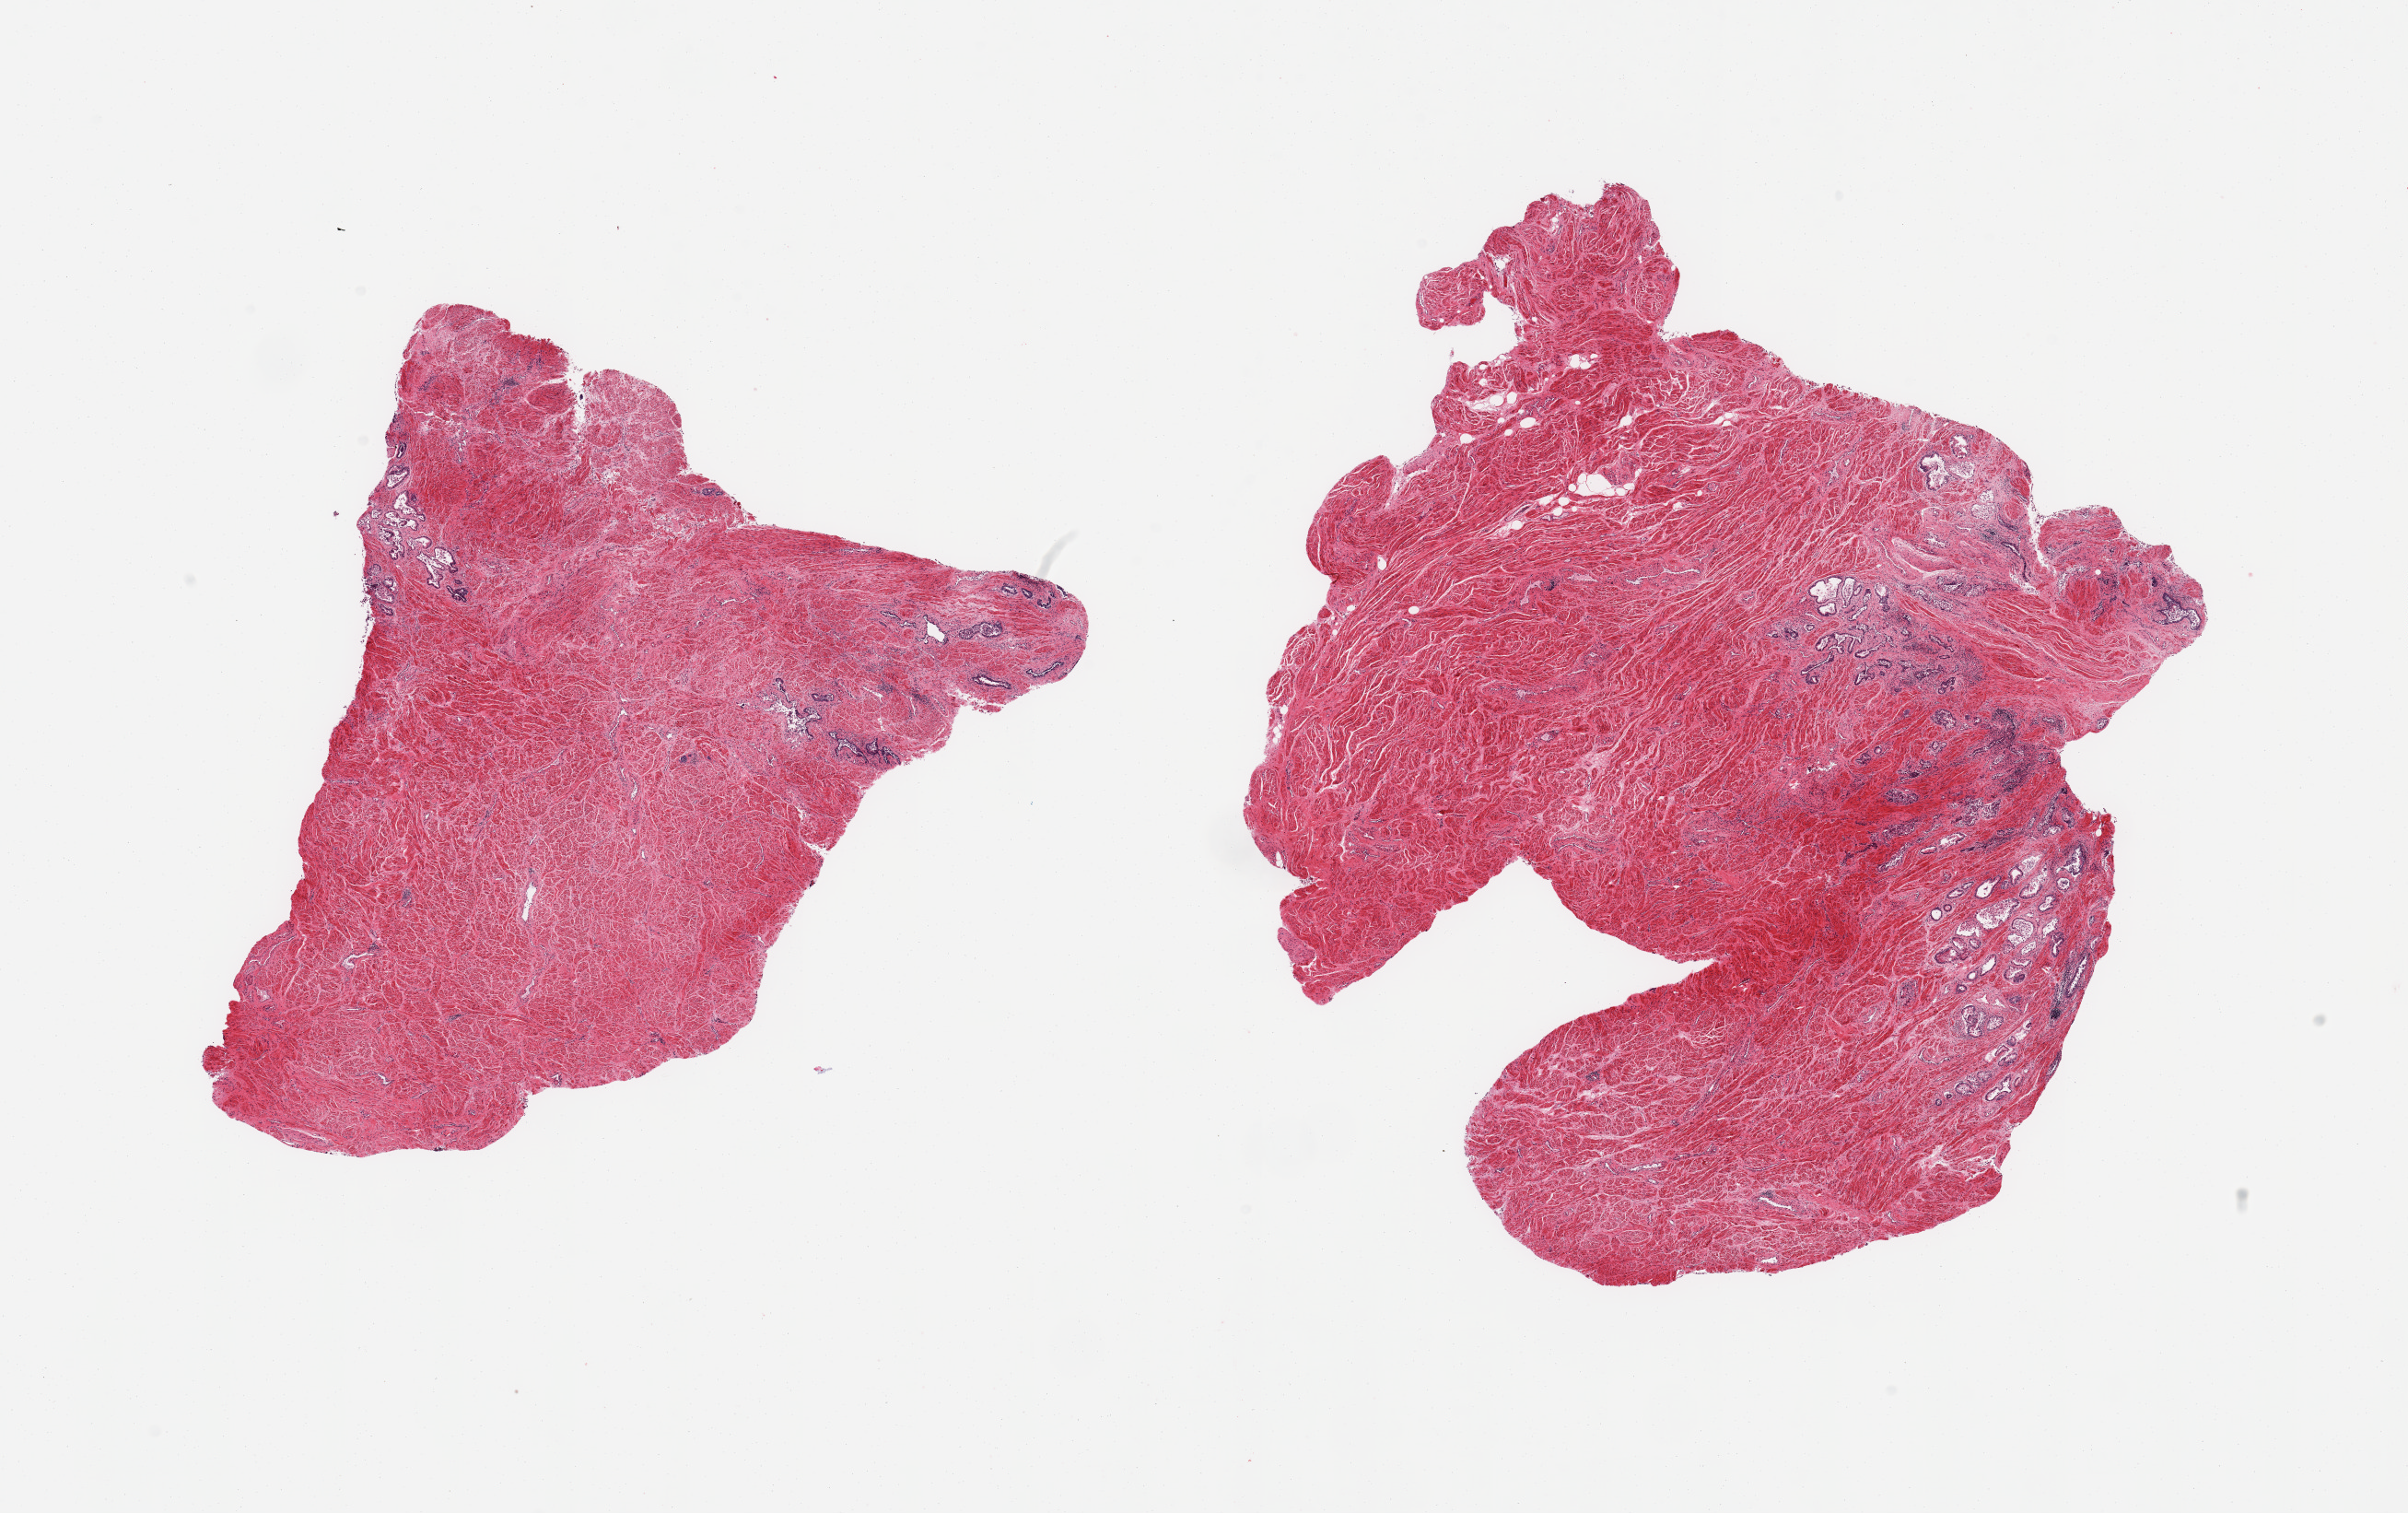
Hematoxylin and eosin (H&E) whole-slide image — whole scanned area (about 20.7 x 13.0 mm, acquisition: 20x scan) shown as a low-resolution overview; PAXgene-fixed paraffin-embedded (PFPE) section; section of prostate (target tissue); donor tissue sample.
Pathologist's review note for this sample: 2 pieces, mainly stroma; glandular elements moderately-markedly autolyzed.